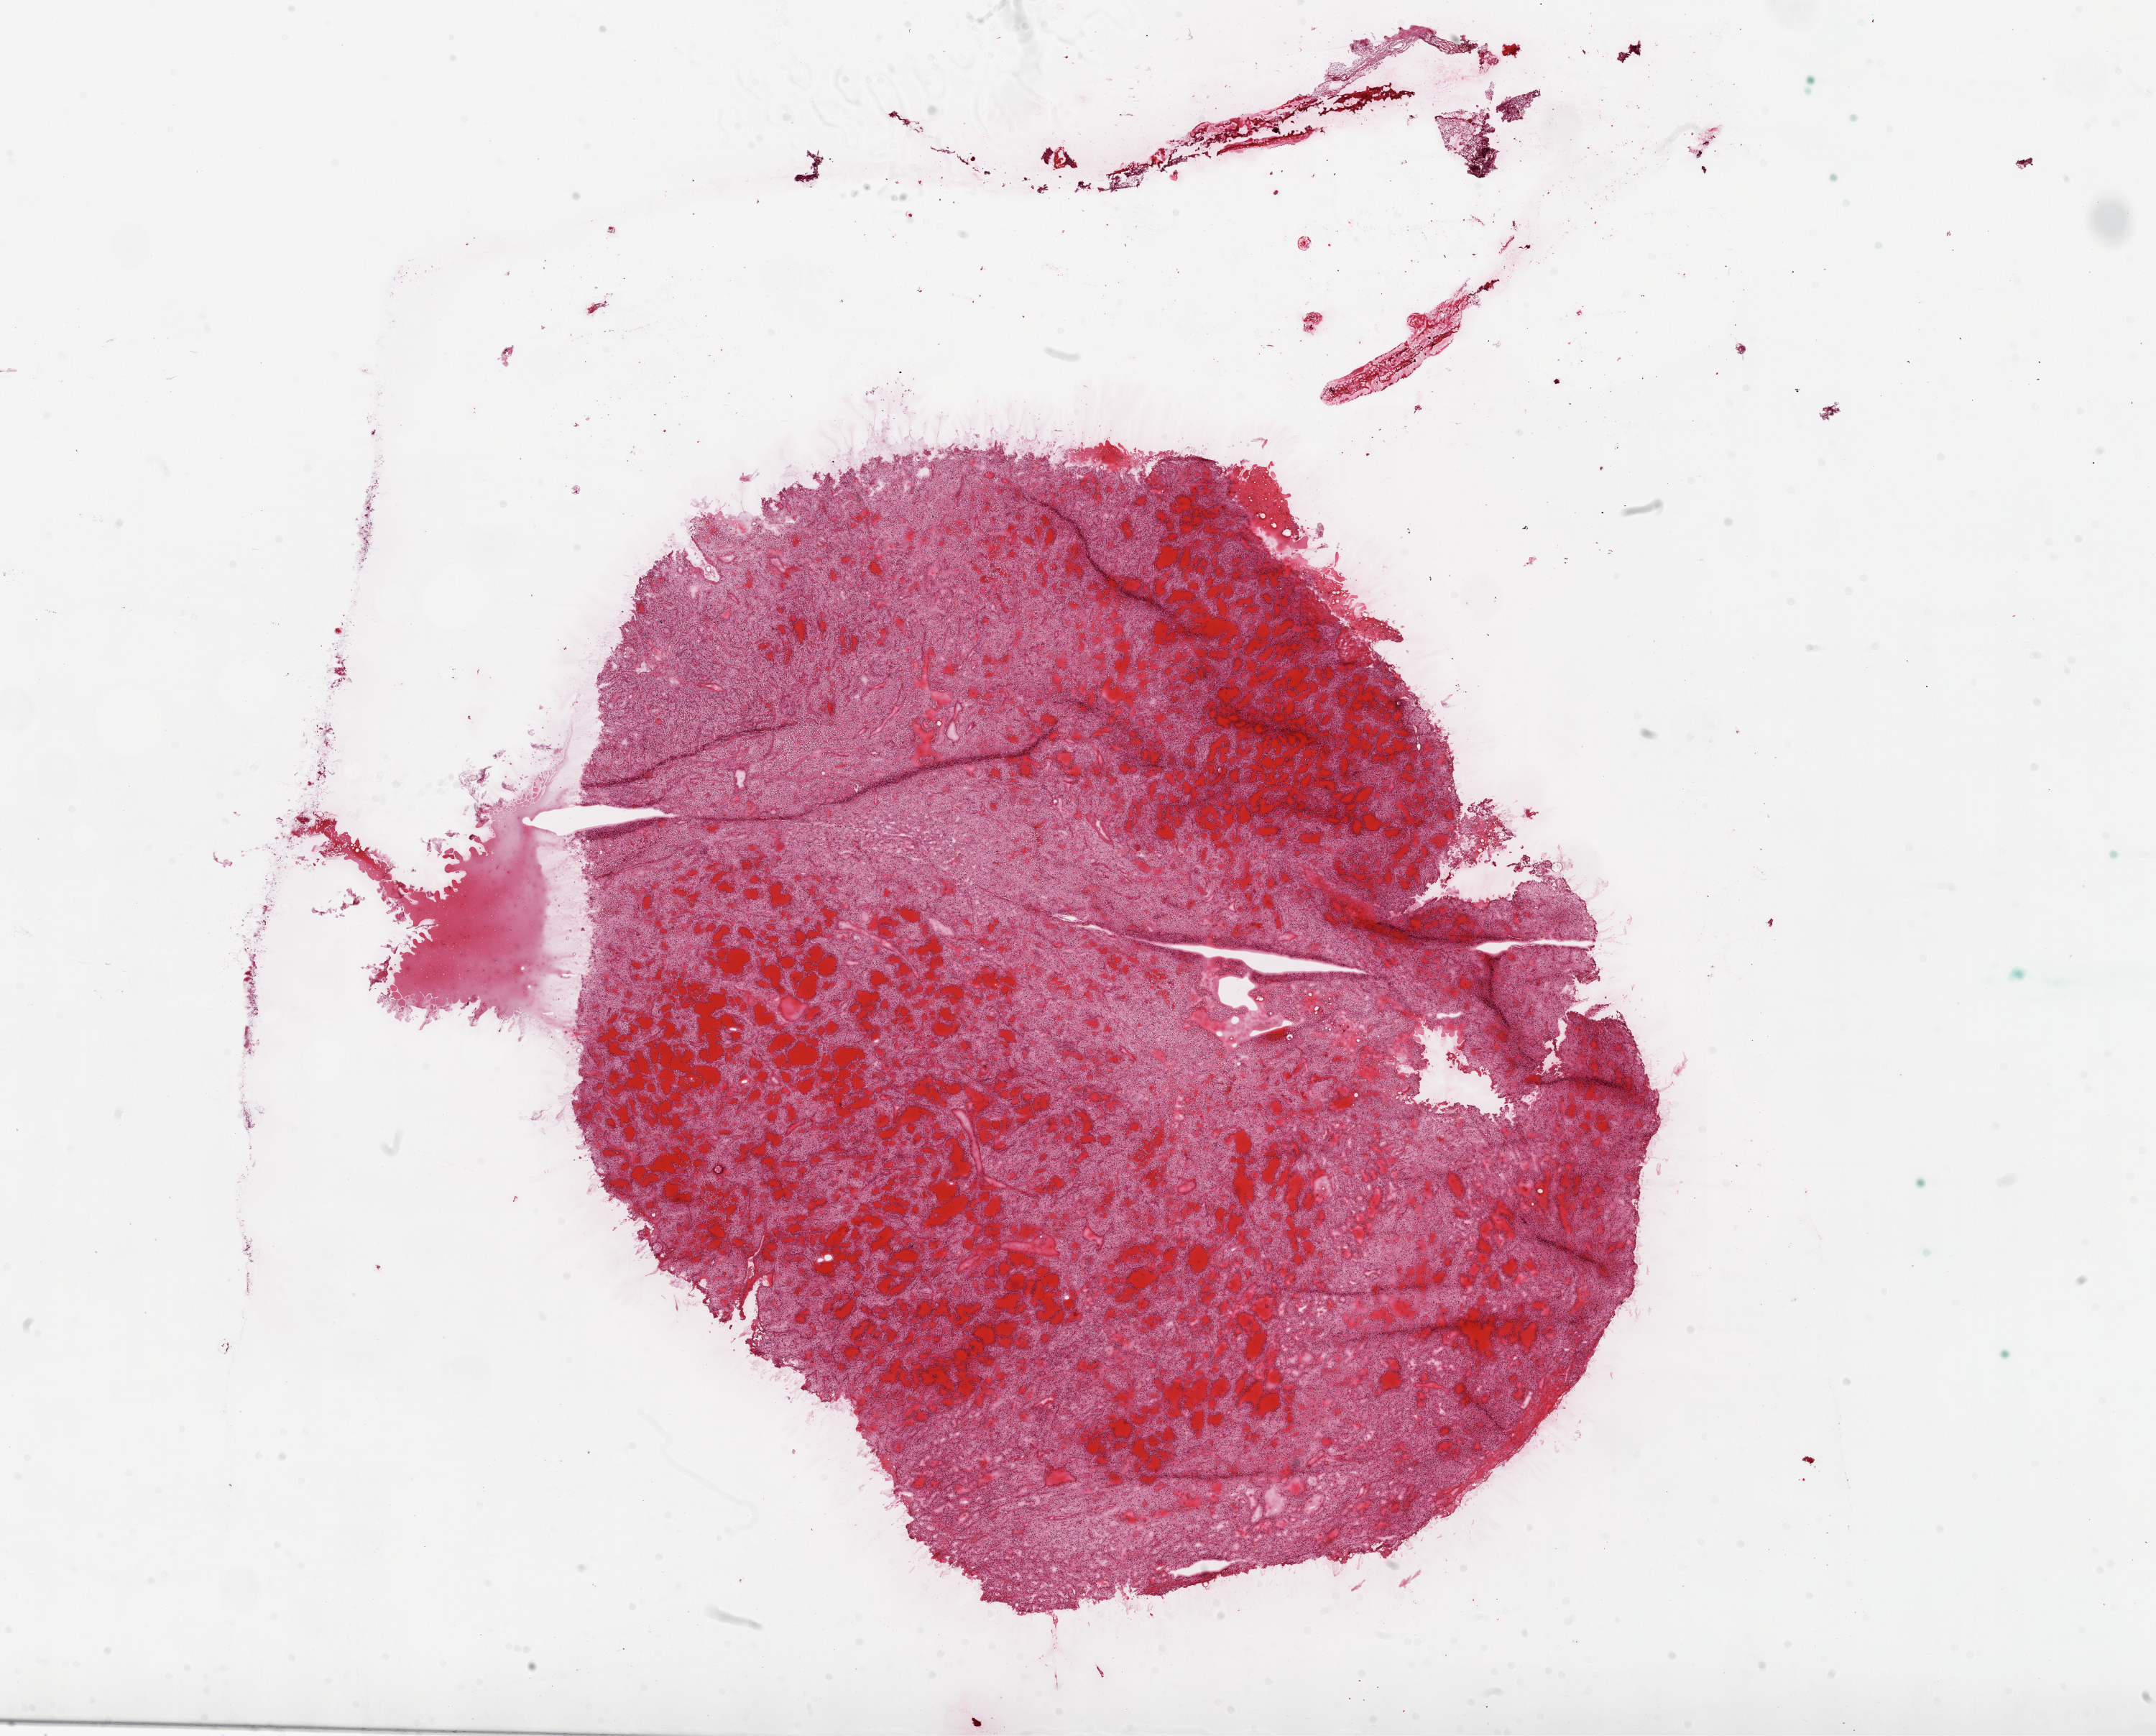
Digitized H&E tissue section (whole slide) — low-resolution overview of the scanned area, about 24.1 x 19.4 mm, frozen section from the top of the tissue portion, sample: primary tumour, kidney. Male patient; age at initial diagnosis 57 years.
Histologic diagnosis: Clear cell adenocarcinoma, NOS.